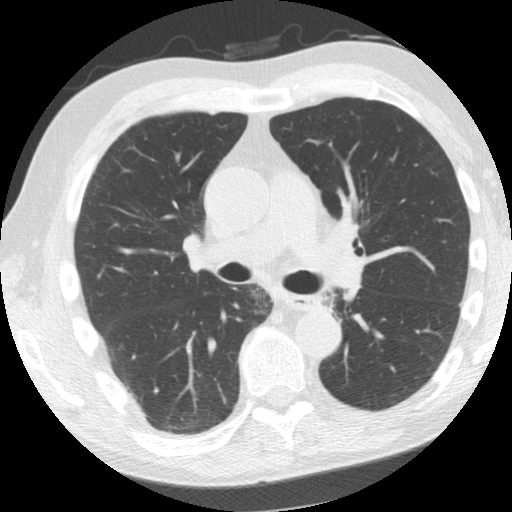
Chest CT (low-dose screening protocol), one axial image, second annual screen, lung window (W 1500 / L -600 HU), 2.5 mm slice thickness, standard (soft-tissue) reconstruction kernel (STANDARD), slice 66 of 156 in the series. Male, age 61 years at enrolment. Former smoker at enrolment.
Expert-annotated lung lesion, bounding box (x1, y1, x2, y2) in pixels: (307, 286, 349, 321). Screening reader's record for this exam: no non-calcified nodule ≥4 mm recorded. Lung cancer was diagnosed 775 days after this screen (after the third annual screen): squamous cell carcinoma, NOS, left upper lobe, left lower lobe, well differentiated (G1), stage IIB (AJCC 6th edition), 100 mm at pathology.